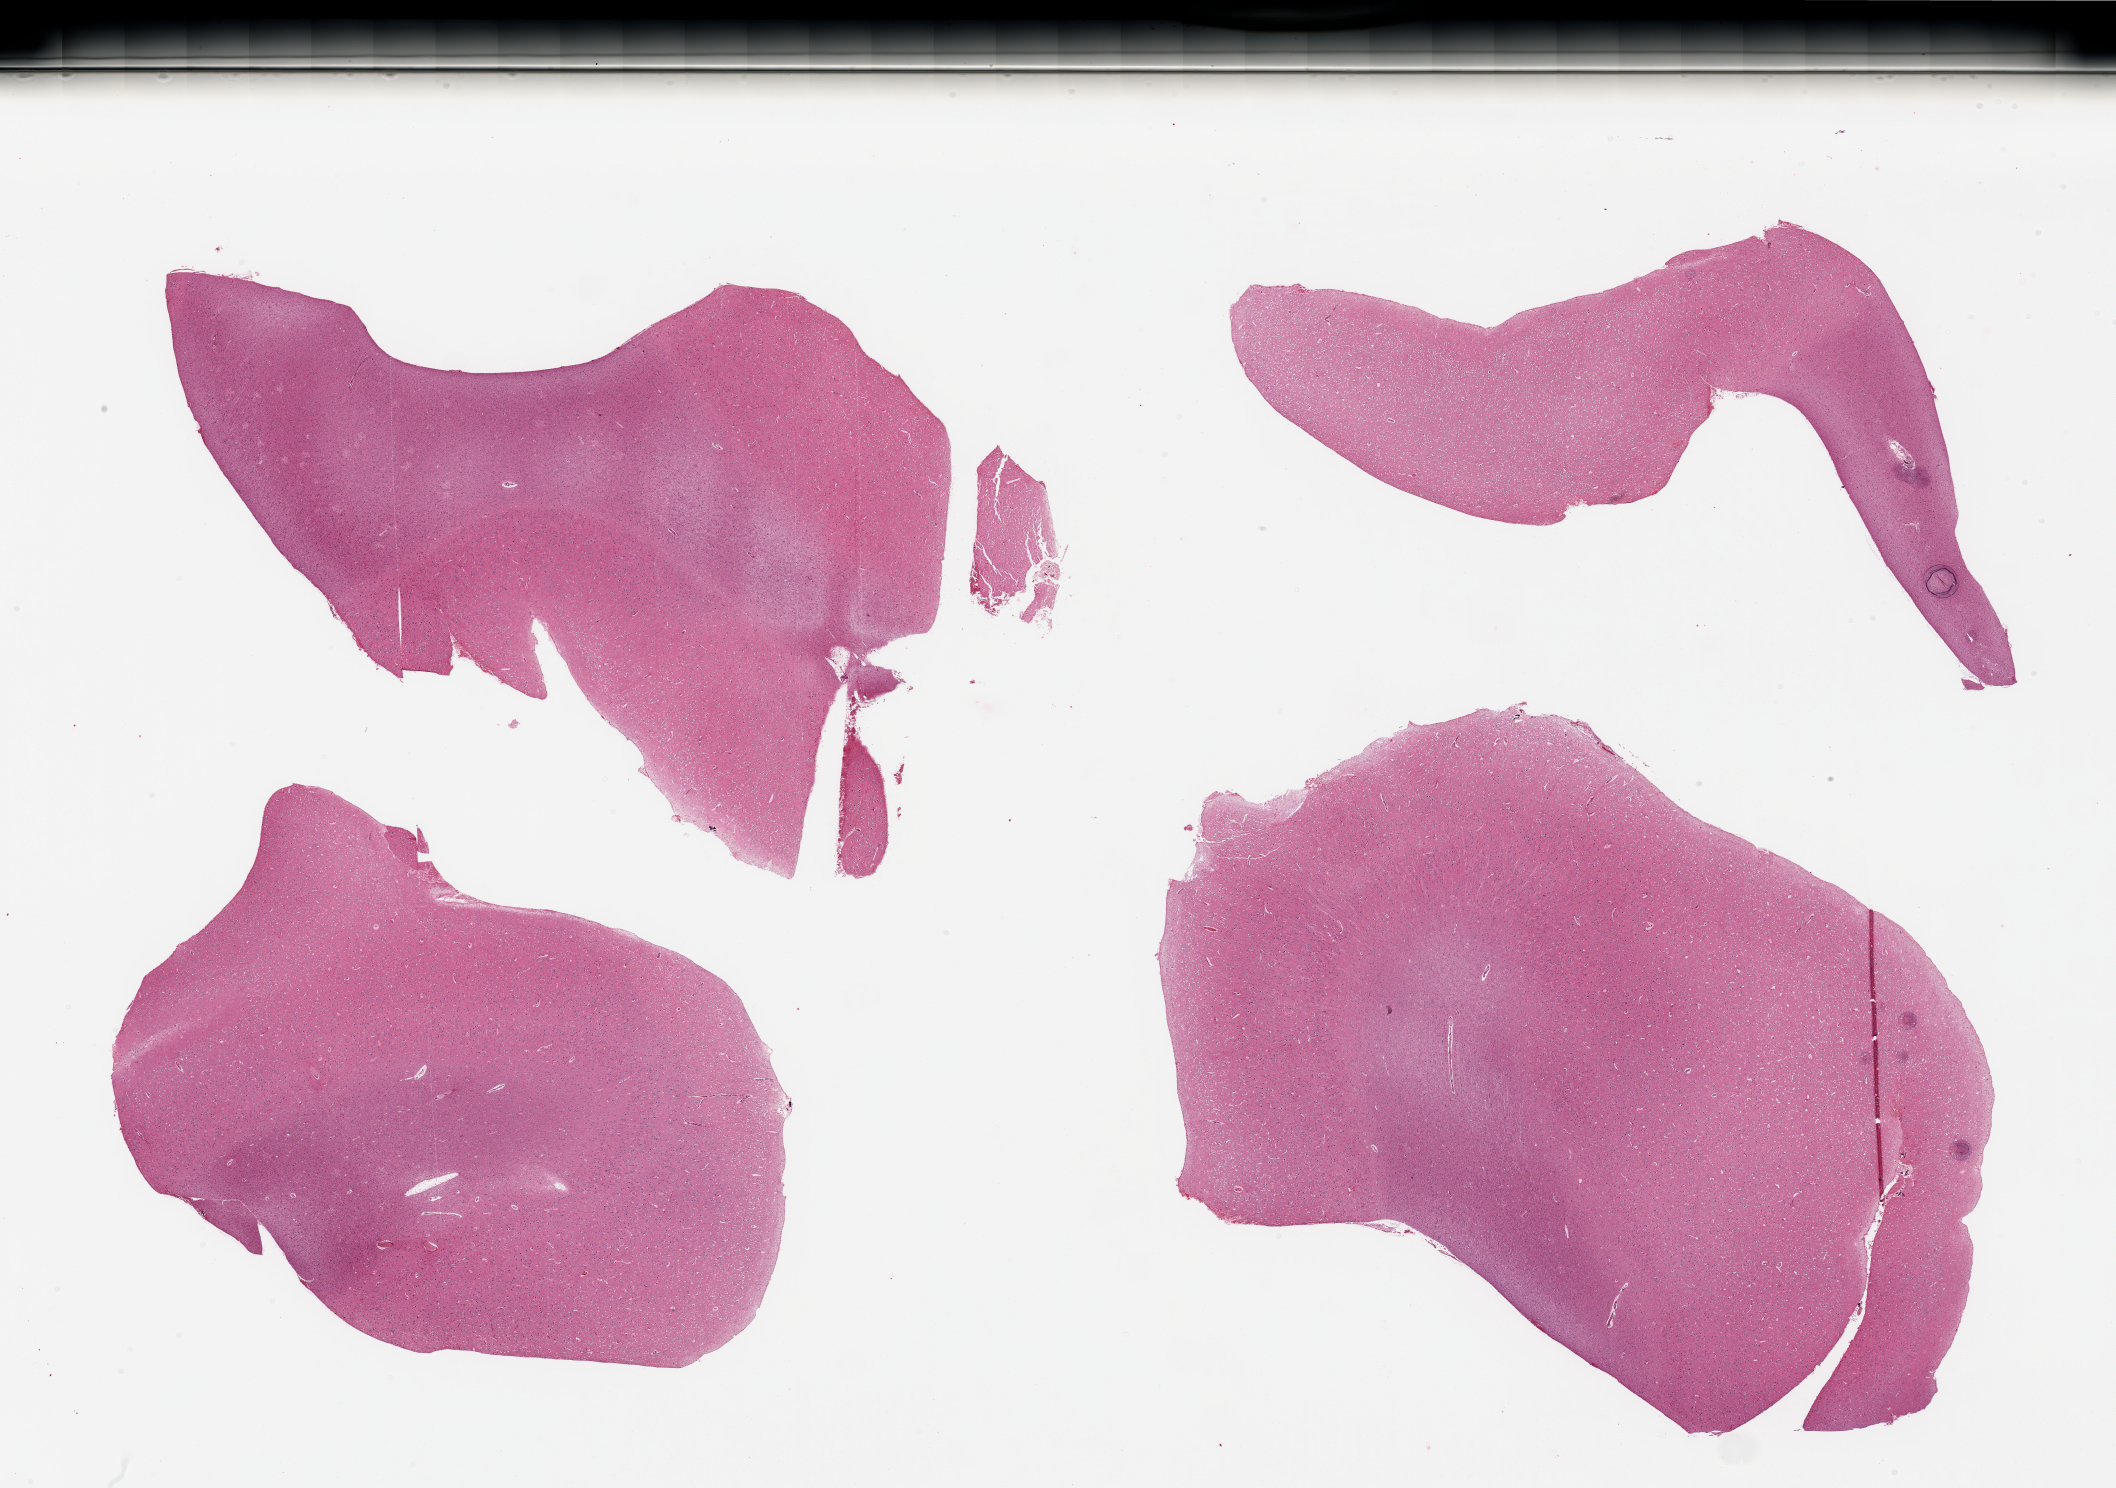
Hematoxylin and eosin (H&E) whole-slide image, brightfield, shown as a low-resolution overview of the whole scanned area (about 33.5 x 23.5 mm), PAXgene-fixed, paraffin-embedded tissue, target tissue: cerebral cortex, donor tissue sample. Donor sex: male.
Reviewer comment on this tissue sample: 4 pieces, no abnormalities.